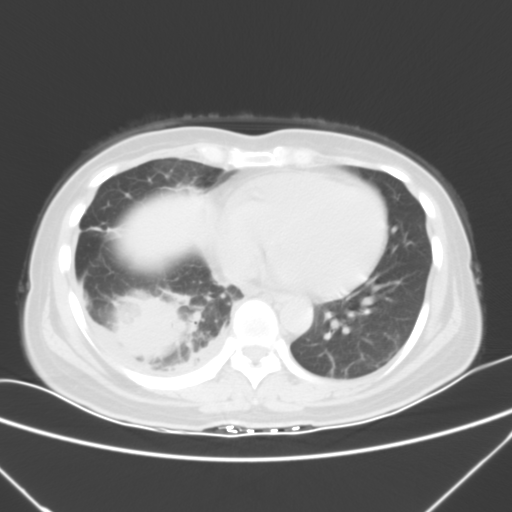
Chest CT, one axial slice; slice 16 of 53 in the series (ordered by position); 120 kVp; lung window (W 1500 / L -600 HU); 5 mm slice thickness; 512 × 512 image matrix. Female patient, age 42 years. Case-level facts recorded for this patient, not image findings: clinical TNM (as recorded): T3 N0 M1c.
Annotated regions visible in this slice (rectangle marked by the reading radiologist):
- lung tumour (recorded histology: adenocarcinoma): bounding box <112,289,190,364> (left, top, right, bottom; pixels)